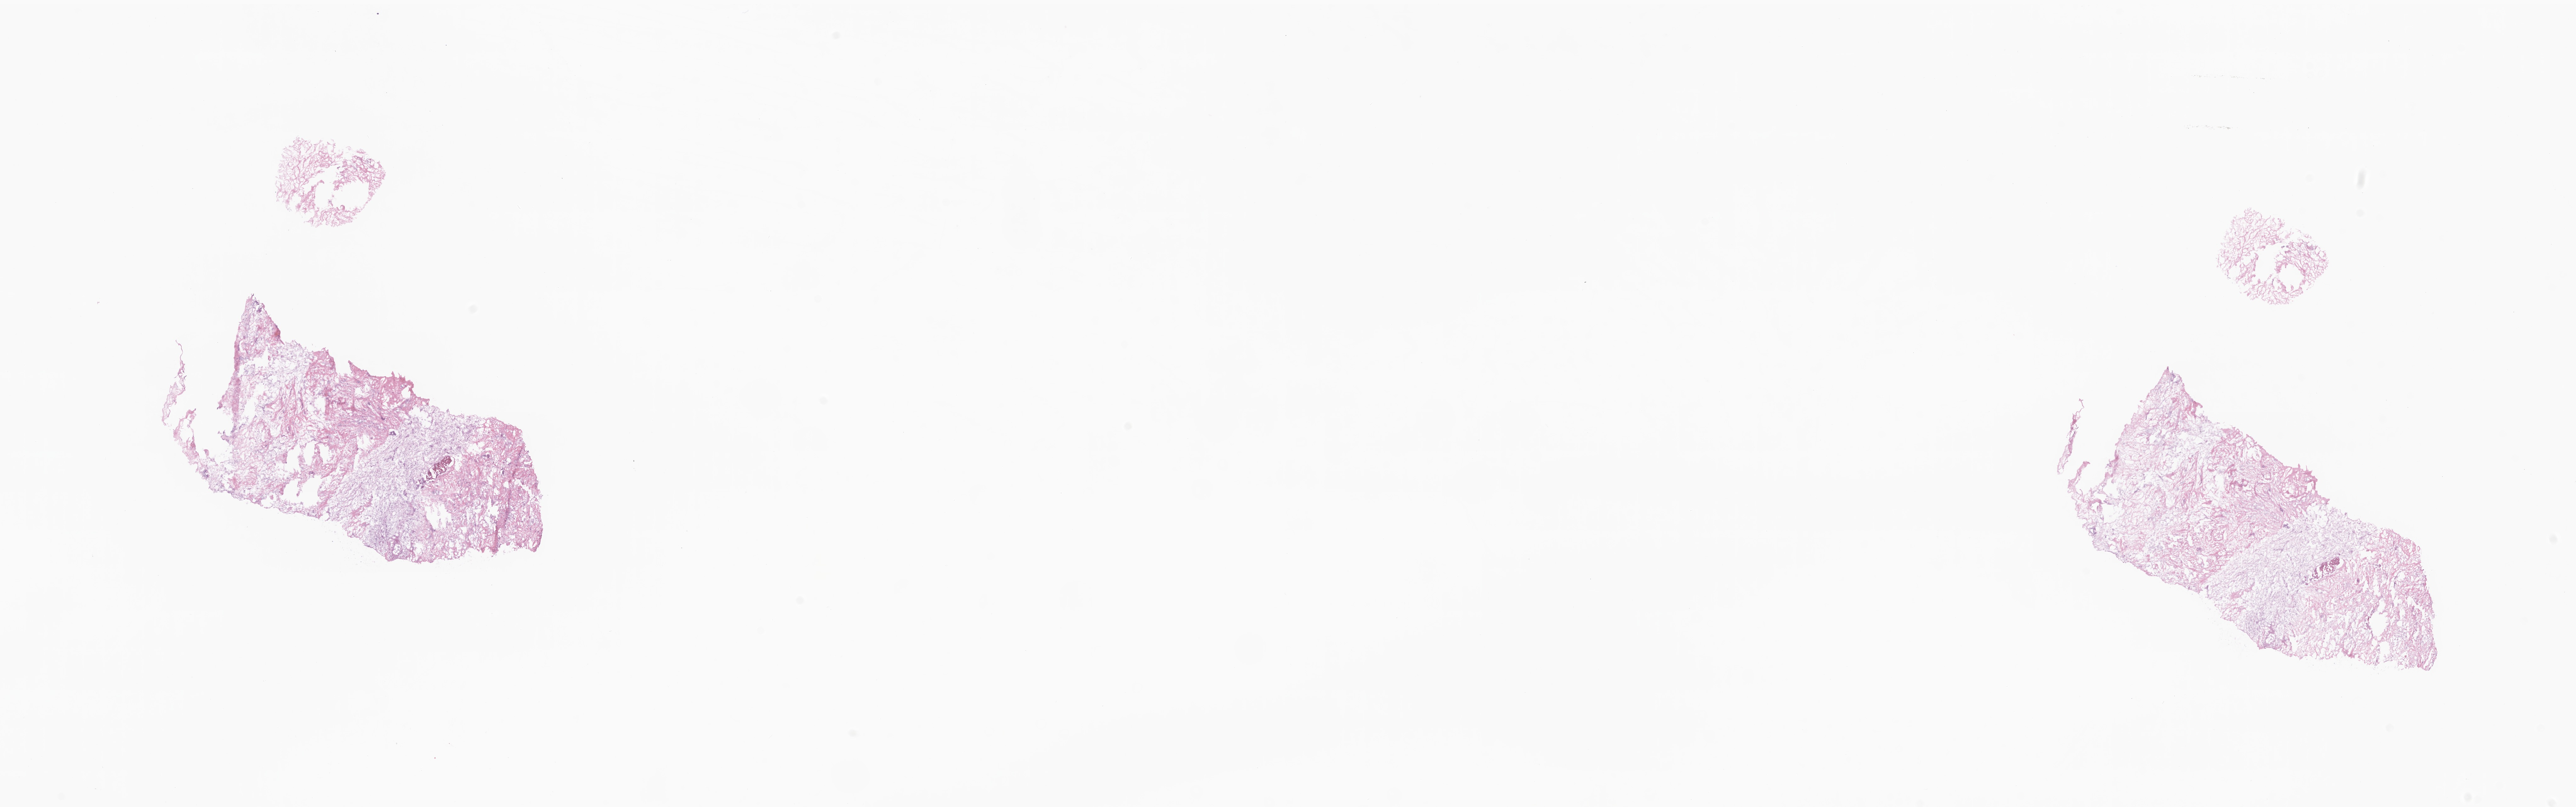
Digitized H&E-stained section — low-resolution overview of the scanned area, about 34.5 x 10.8 mm. Frozen section (tissue freezing medium). Primary tumor. Anatomic site: breast (right). Female patient; age at initial diagnosis 69 years. Pathologist review of this section (percent, as recorded): tumor cells 90%, tumor nuclei 75%, stromal cells 0%, necrosis 0%, normal cells 10%. Infiltration values recorded for this section: lymphocyte infiltration 0%, monocyte infiltration 0%, neutrophil infiltration 0%.
Histologic diagnosis: Infiltrating duct carcinoma, NOS.